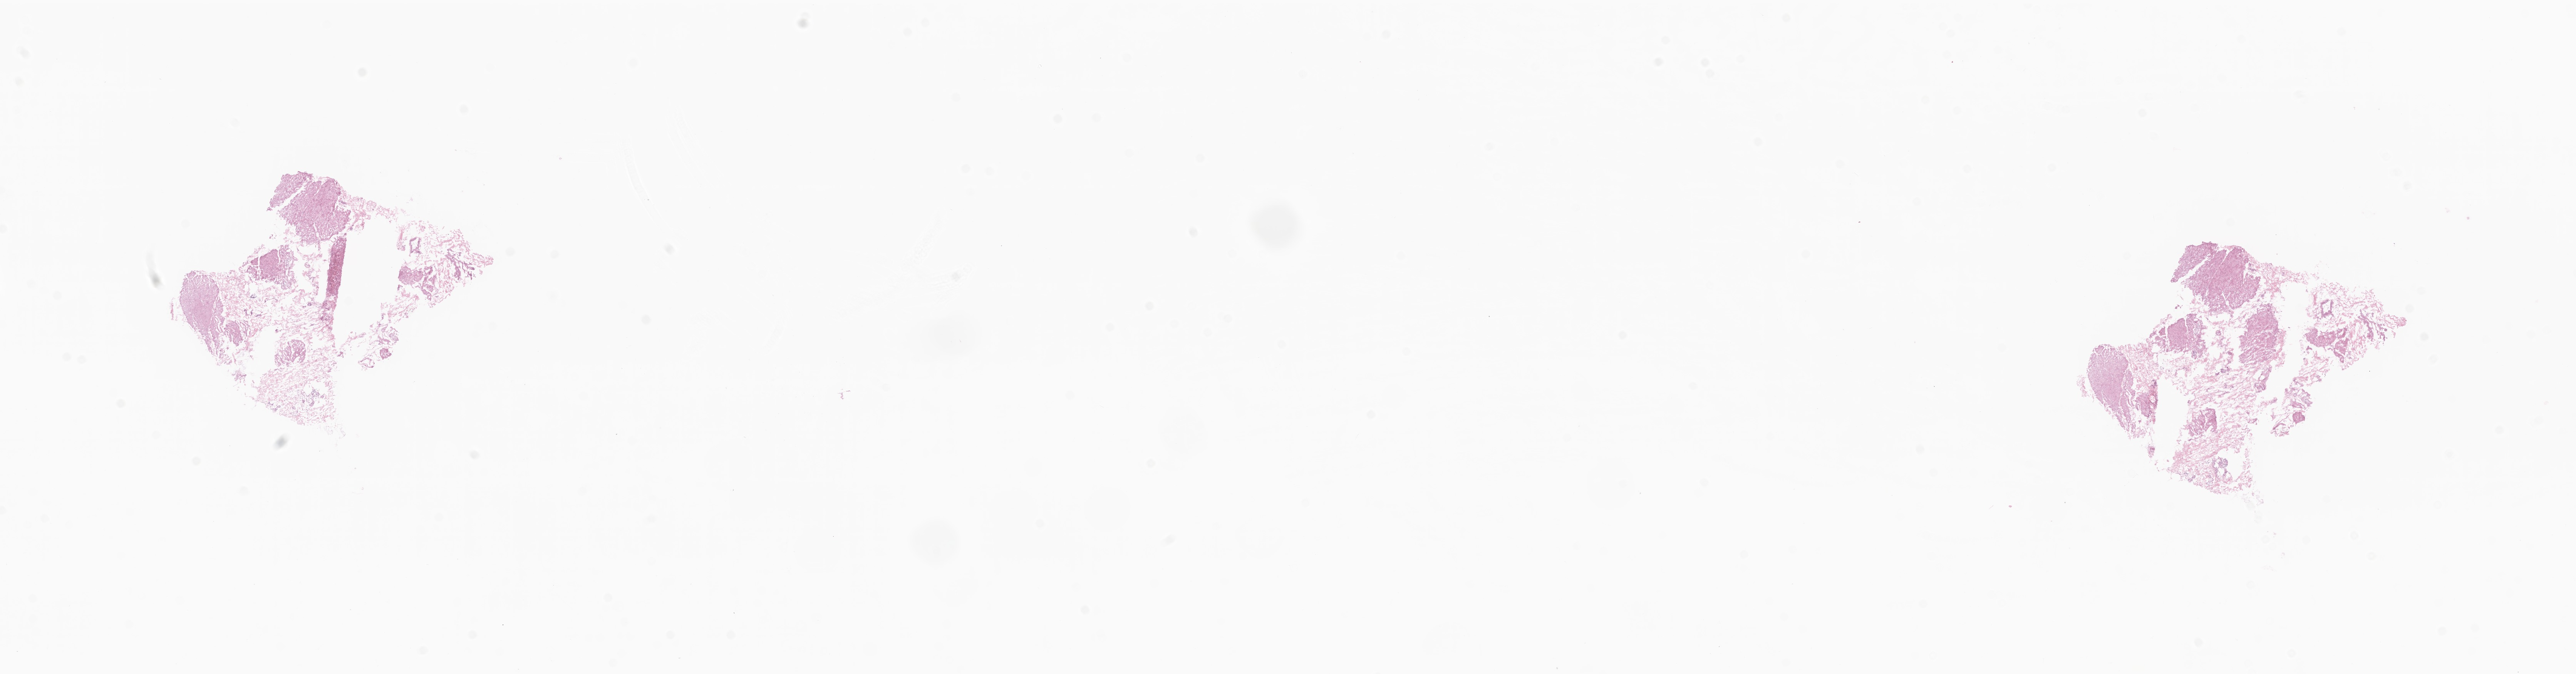
Whole-slide image, hematoxylin and eosin (H&E) stain, shown as a low-resolution overview of the whole scanned area (about 28.2 x 7.4 mm); frozen section (tissue freezing medium); normal-tissue sample (non-tumor) from a patient with adenocarcinoma, NOS; anatomic site: rectum. Patient sex: male. Pathologist review of this section (percent, as recorded): tumor cells 0%, tumor nuclei 0%, stromal cells 0%, necrosis 0%, normal cells 100%. Infiltration values recorded for this section: lymphocyte infiltration 0%, monocyte infiltration 0%, neutrophil infiltration 0%.
• this section: non-tumor tissue sample; the patient's diagnosis is given above